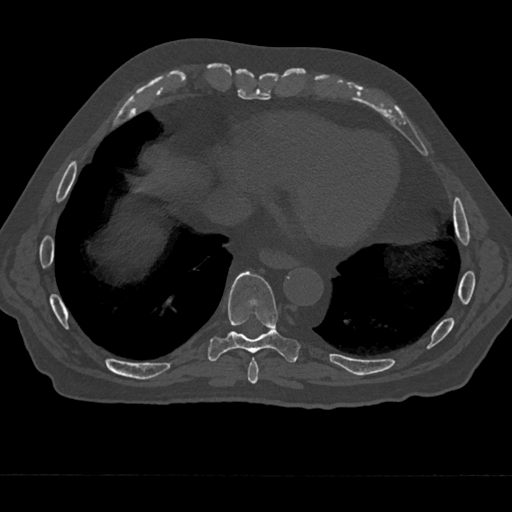
CT including the spine, one axial slice. Position 264 of 797 along the scan axis. Bone window (W 1800 / L 400 HU). 512 × 512 image matrix, field of view 377 × 377 mm. Male patient, age 75 years. Case-level facts recorded for this patient, not image findings: primary cancer: renal; vertebrae with lytic lesions (as recorded): T4.
Outlined on this slice (semi-automatic segmentation, software-assisted and operator-edited):
- T8 vertebra: box from (x=247, y=357) to (x=259, y=384) px
- T9 vertebra: (x=207, y=271)–(x=301, y=363)